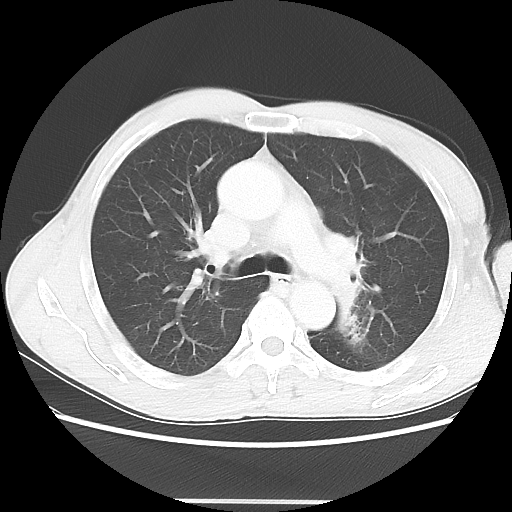
Chest CT, one axial slice. Slice 42 of 62 in the series (ordered by position). Reconstruction kernel LUNG. Lung window (W 1500 / L -600 HU). 5 mm slice thickness. 512 × 512 image matrix, field of view 360 × 360 mm. Patient: male, 61 years. From the clinical record (not read from this slice): clinical TNM (as recorded): T3 N1 M1.
Structures marked on this image (bounding box drawn by a radiologist):
- lung tumour (recorded histology: adenocarcinoma): bounding box (x1, y1, x2, y2) in pixels: (328, 221, 380, 340)